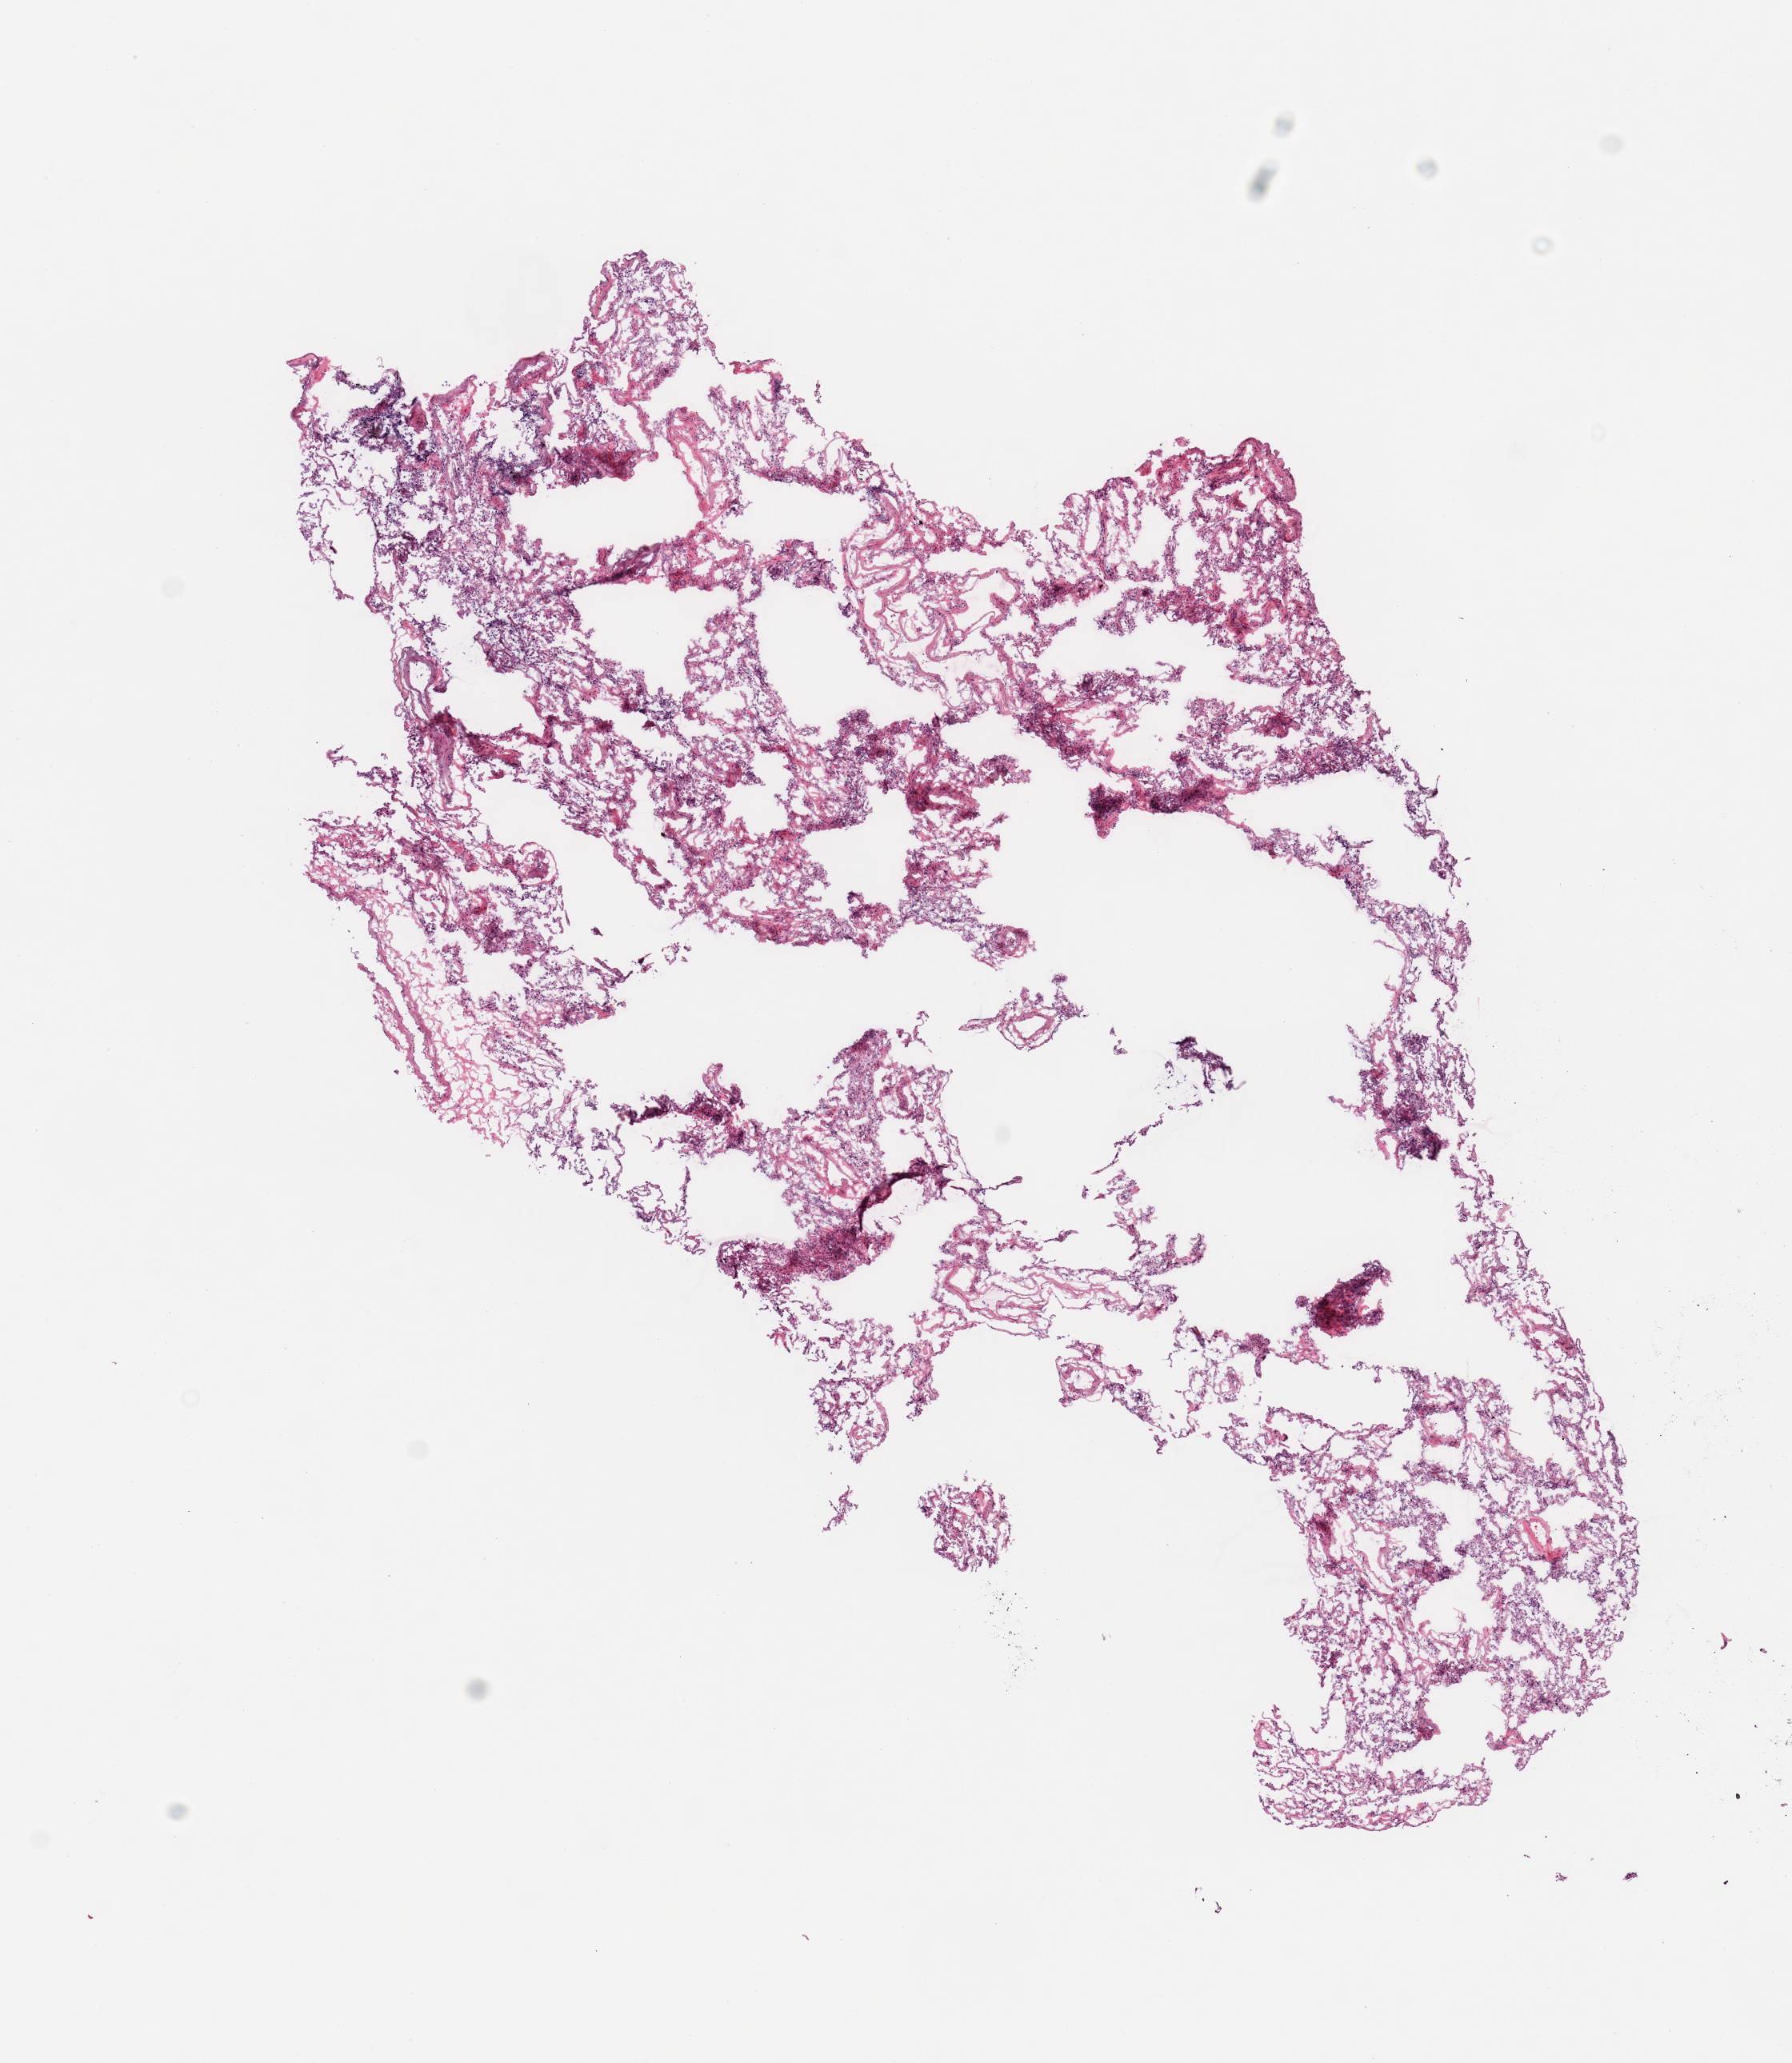
Whole-slide image, hematoxylin and eosin (H&E) stain, whole scanned area (about 8.9 x 10.2 mm) shown as a low-resolution overview. Donor sex: male.
• specimen: frozen section (dry ice); section of lung (target tissue); donor tissue sample